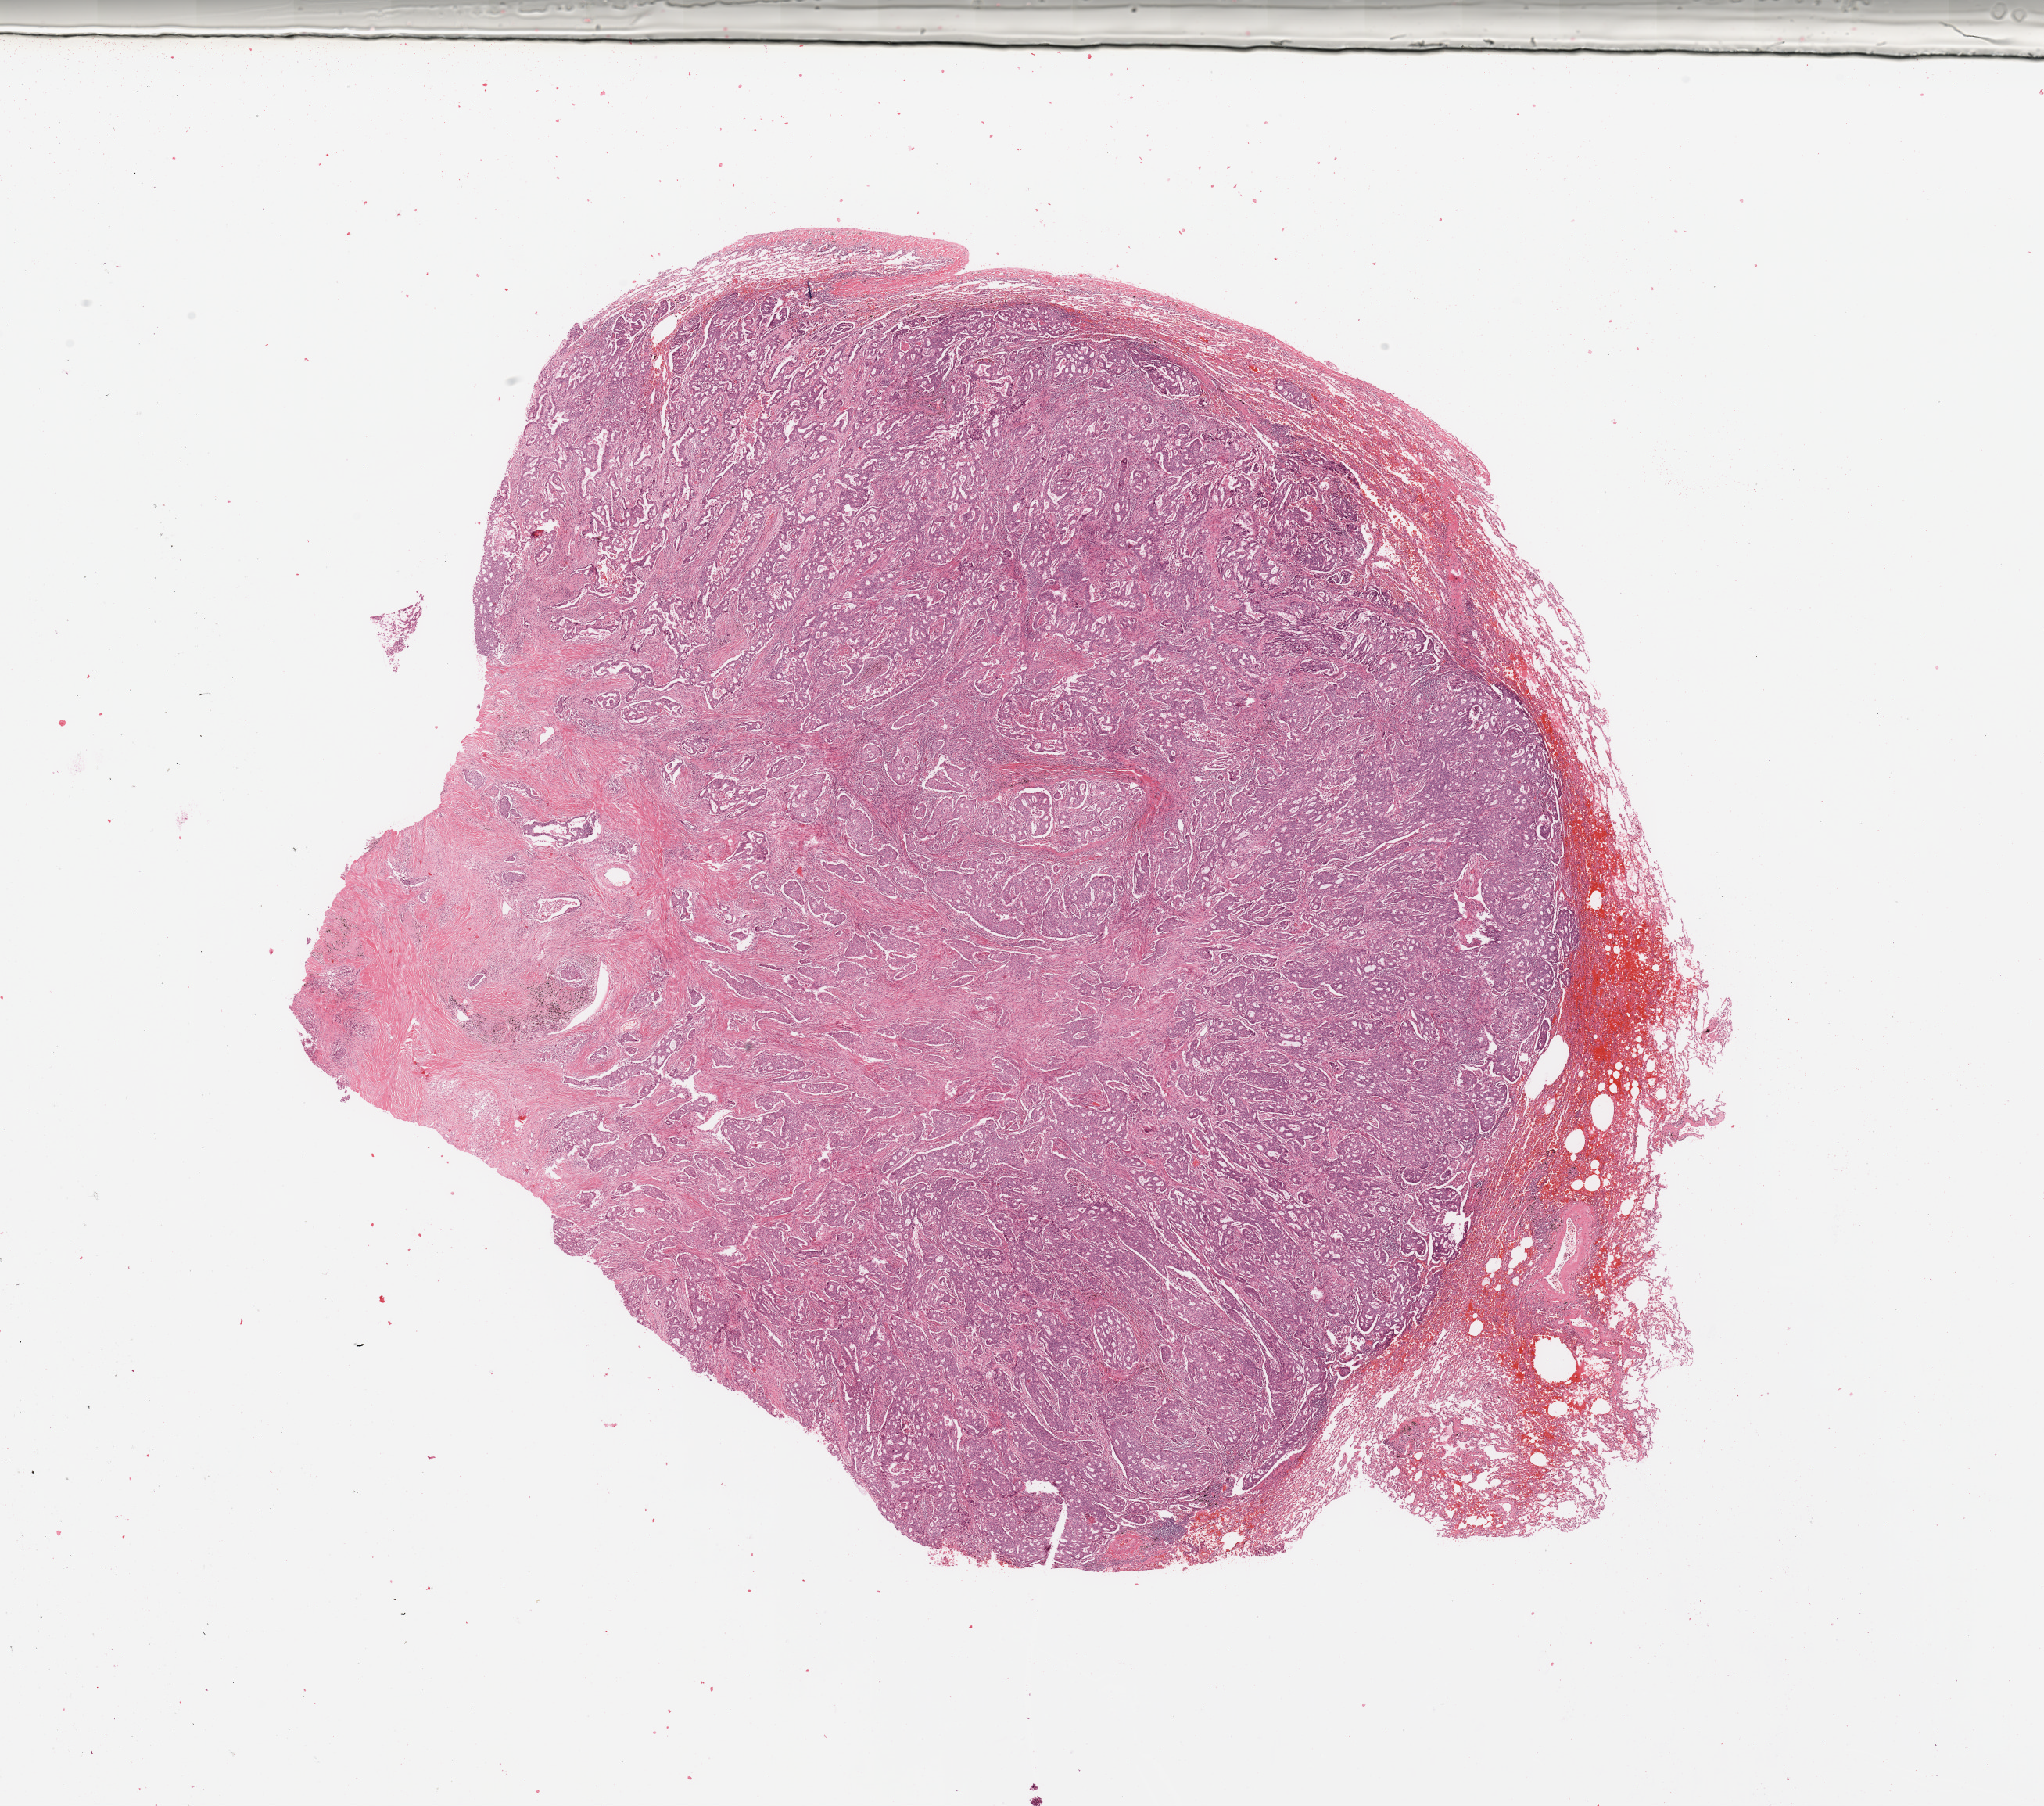
Whole-slide histology image, Hematoxylin and eosin (H&E) stained — a low-resolution overview of the entire scanned area, about 20.7 x 18.3 mm; tumour tissue sample, lung. Male, 67 y/o. Histologic grade: G2 (moderately differentiated).
- AJCC pathologic stage: IB
- histologic diagnosis: Adenocarcinoma, NOS